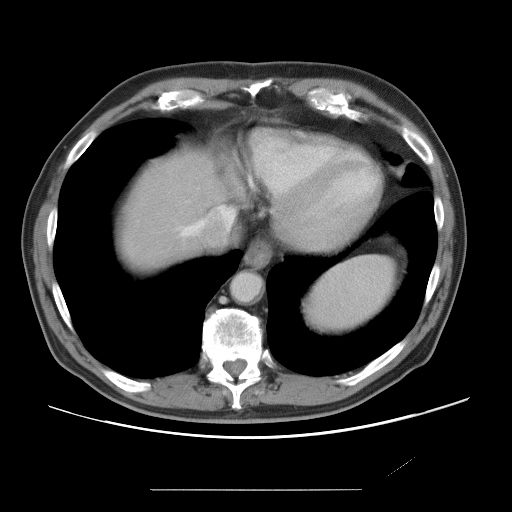
Contrast-enhanced abdominal CT, one axial slice. Position 67 of 87 along the scan axis. 120 kVp. Soft-tissue window (W 400 / L 40 HU). 512 × 512 image matrix, field of view 406 × 406 mm. Male patient, age 74 years. Case-level facts recorded for this patient, not image findings: diagnosis: colorectal cancer liver metastases, imaged before liver resection; multiple liver metastases: yes; largest metastasis: 1.1 cm; disease in both lobes: no.
Outlined on this slice (expert manual segmentation):
- hepatic veins: bounding box [x1, y1, x2, y2] px = [182, 226, 195, 236]
- liver: [117, 154, 229, 272]
- planned liver remnant (the part of the liver to remain after resection): [118, 154, 230, 271]